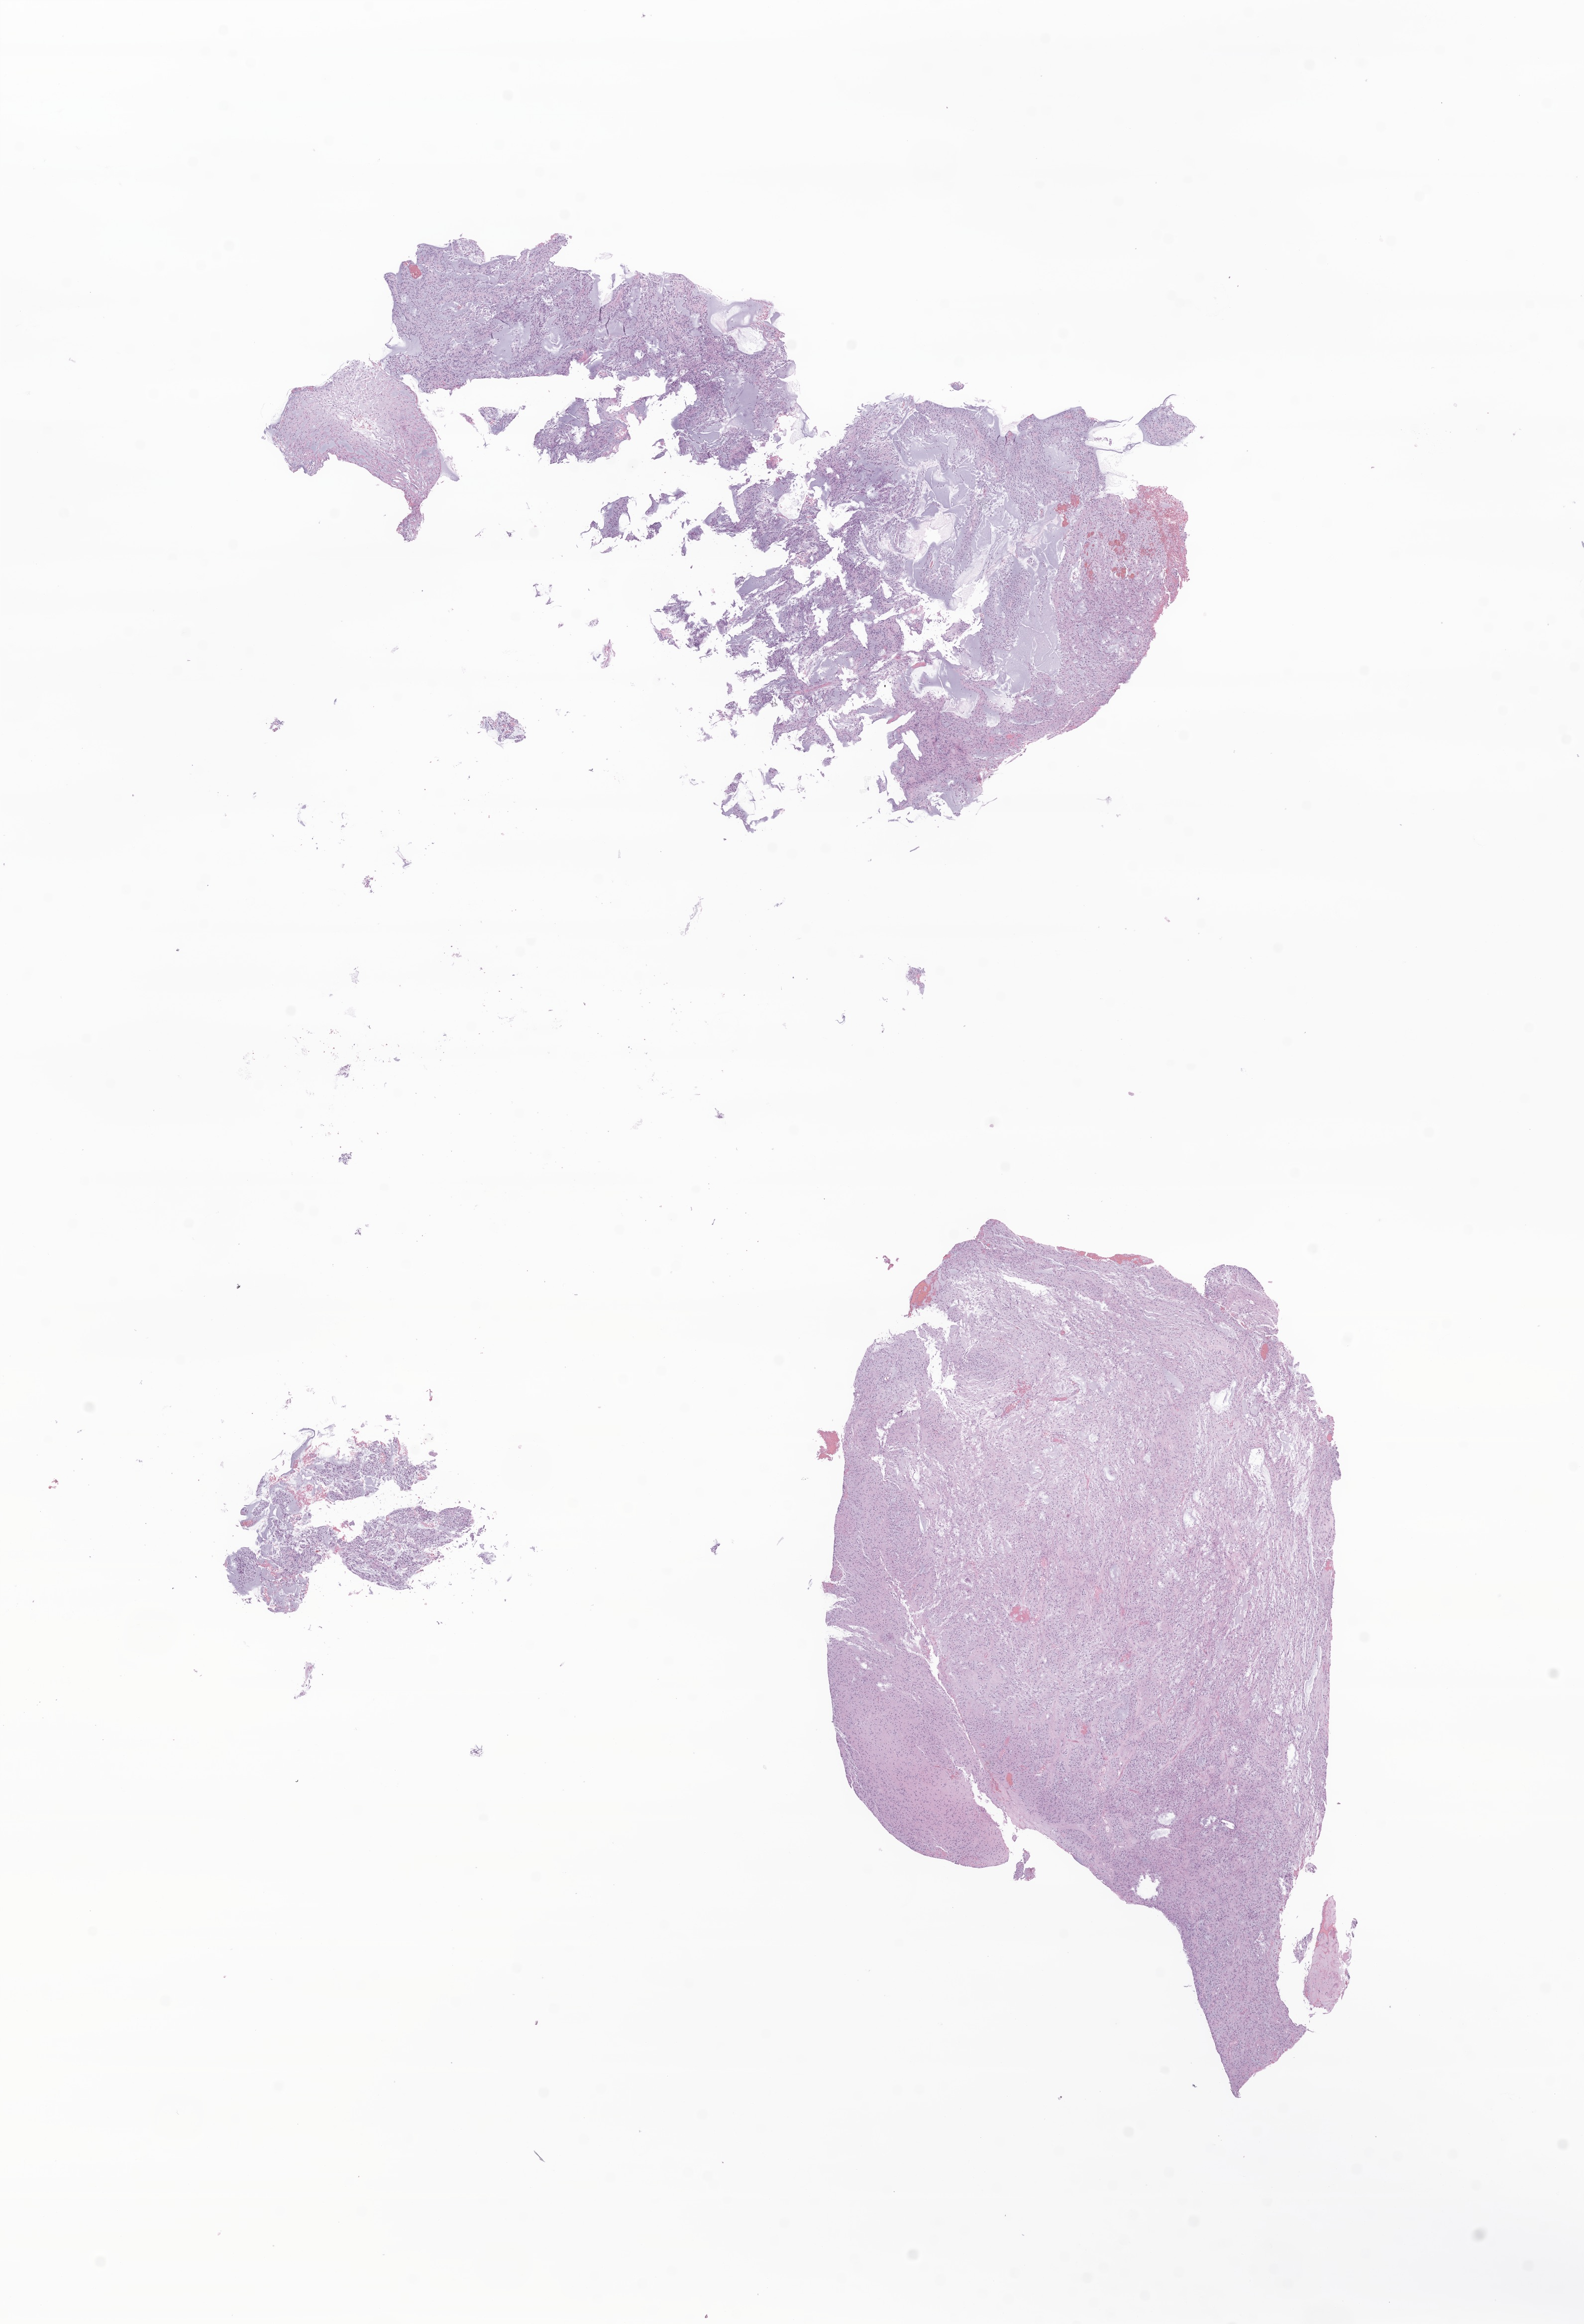
Digitized H&E-stained section of tumor tissue from the brain — shown as a low-resolution overview of the whole scanned area (about 13.4 x 19.7 mm), formalin-fixed paraffin-embedded section. Patient: male, age 151 months (12 years 7 months).
Diagnosis: Glioma, malignant.